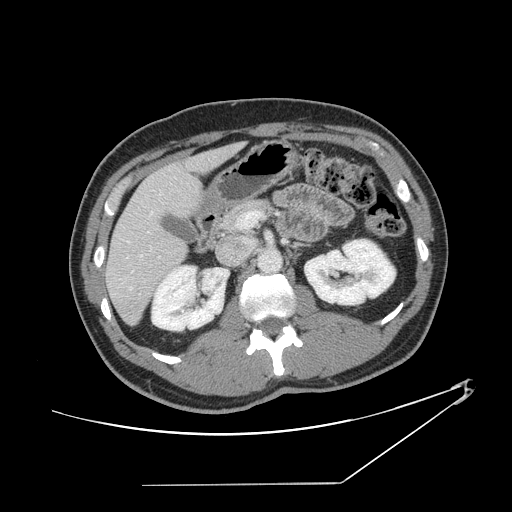
Contrast-enhanced abdominal CT, one axial slice. Slice 70 of 152 in the series (ordered by position). Reconstruction kernel STANDARD. 120 kVp. Soft-tissue window (W 400 / L 40 HU). 2.5 mm slice thickness. 512 × 512 image matrix, field of view 432 × 432 mm. Male patient, age 45 years. From the clinical record (not read from this slice): diagnosis: colorectal cancer liver metastases, imaged before liver resection; multiple liver metastases: no; largest metastasis: 1 cm; disease in both lobes: no.
Outlined on this slice (outlined manually by an expert reader):
- hepatic veins: bounding box [x1, y1, x2, y2] px = [121, 190, 162, 290]
- liver: [107, 145, 239, 324]
- planned liver remnant (the part of the liver to remain after resection): [107, 162, 200, 324]
- portal vein (with intrahepatic branches): [237, 211, 262, 229]